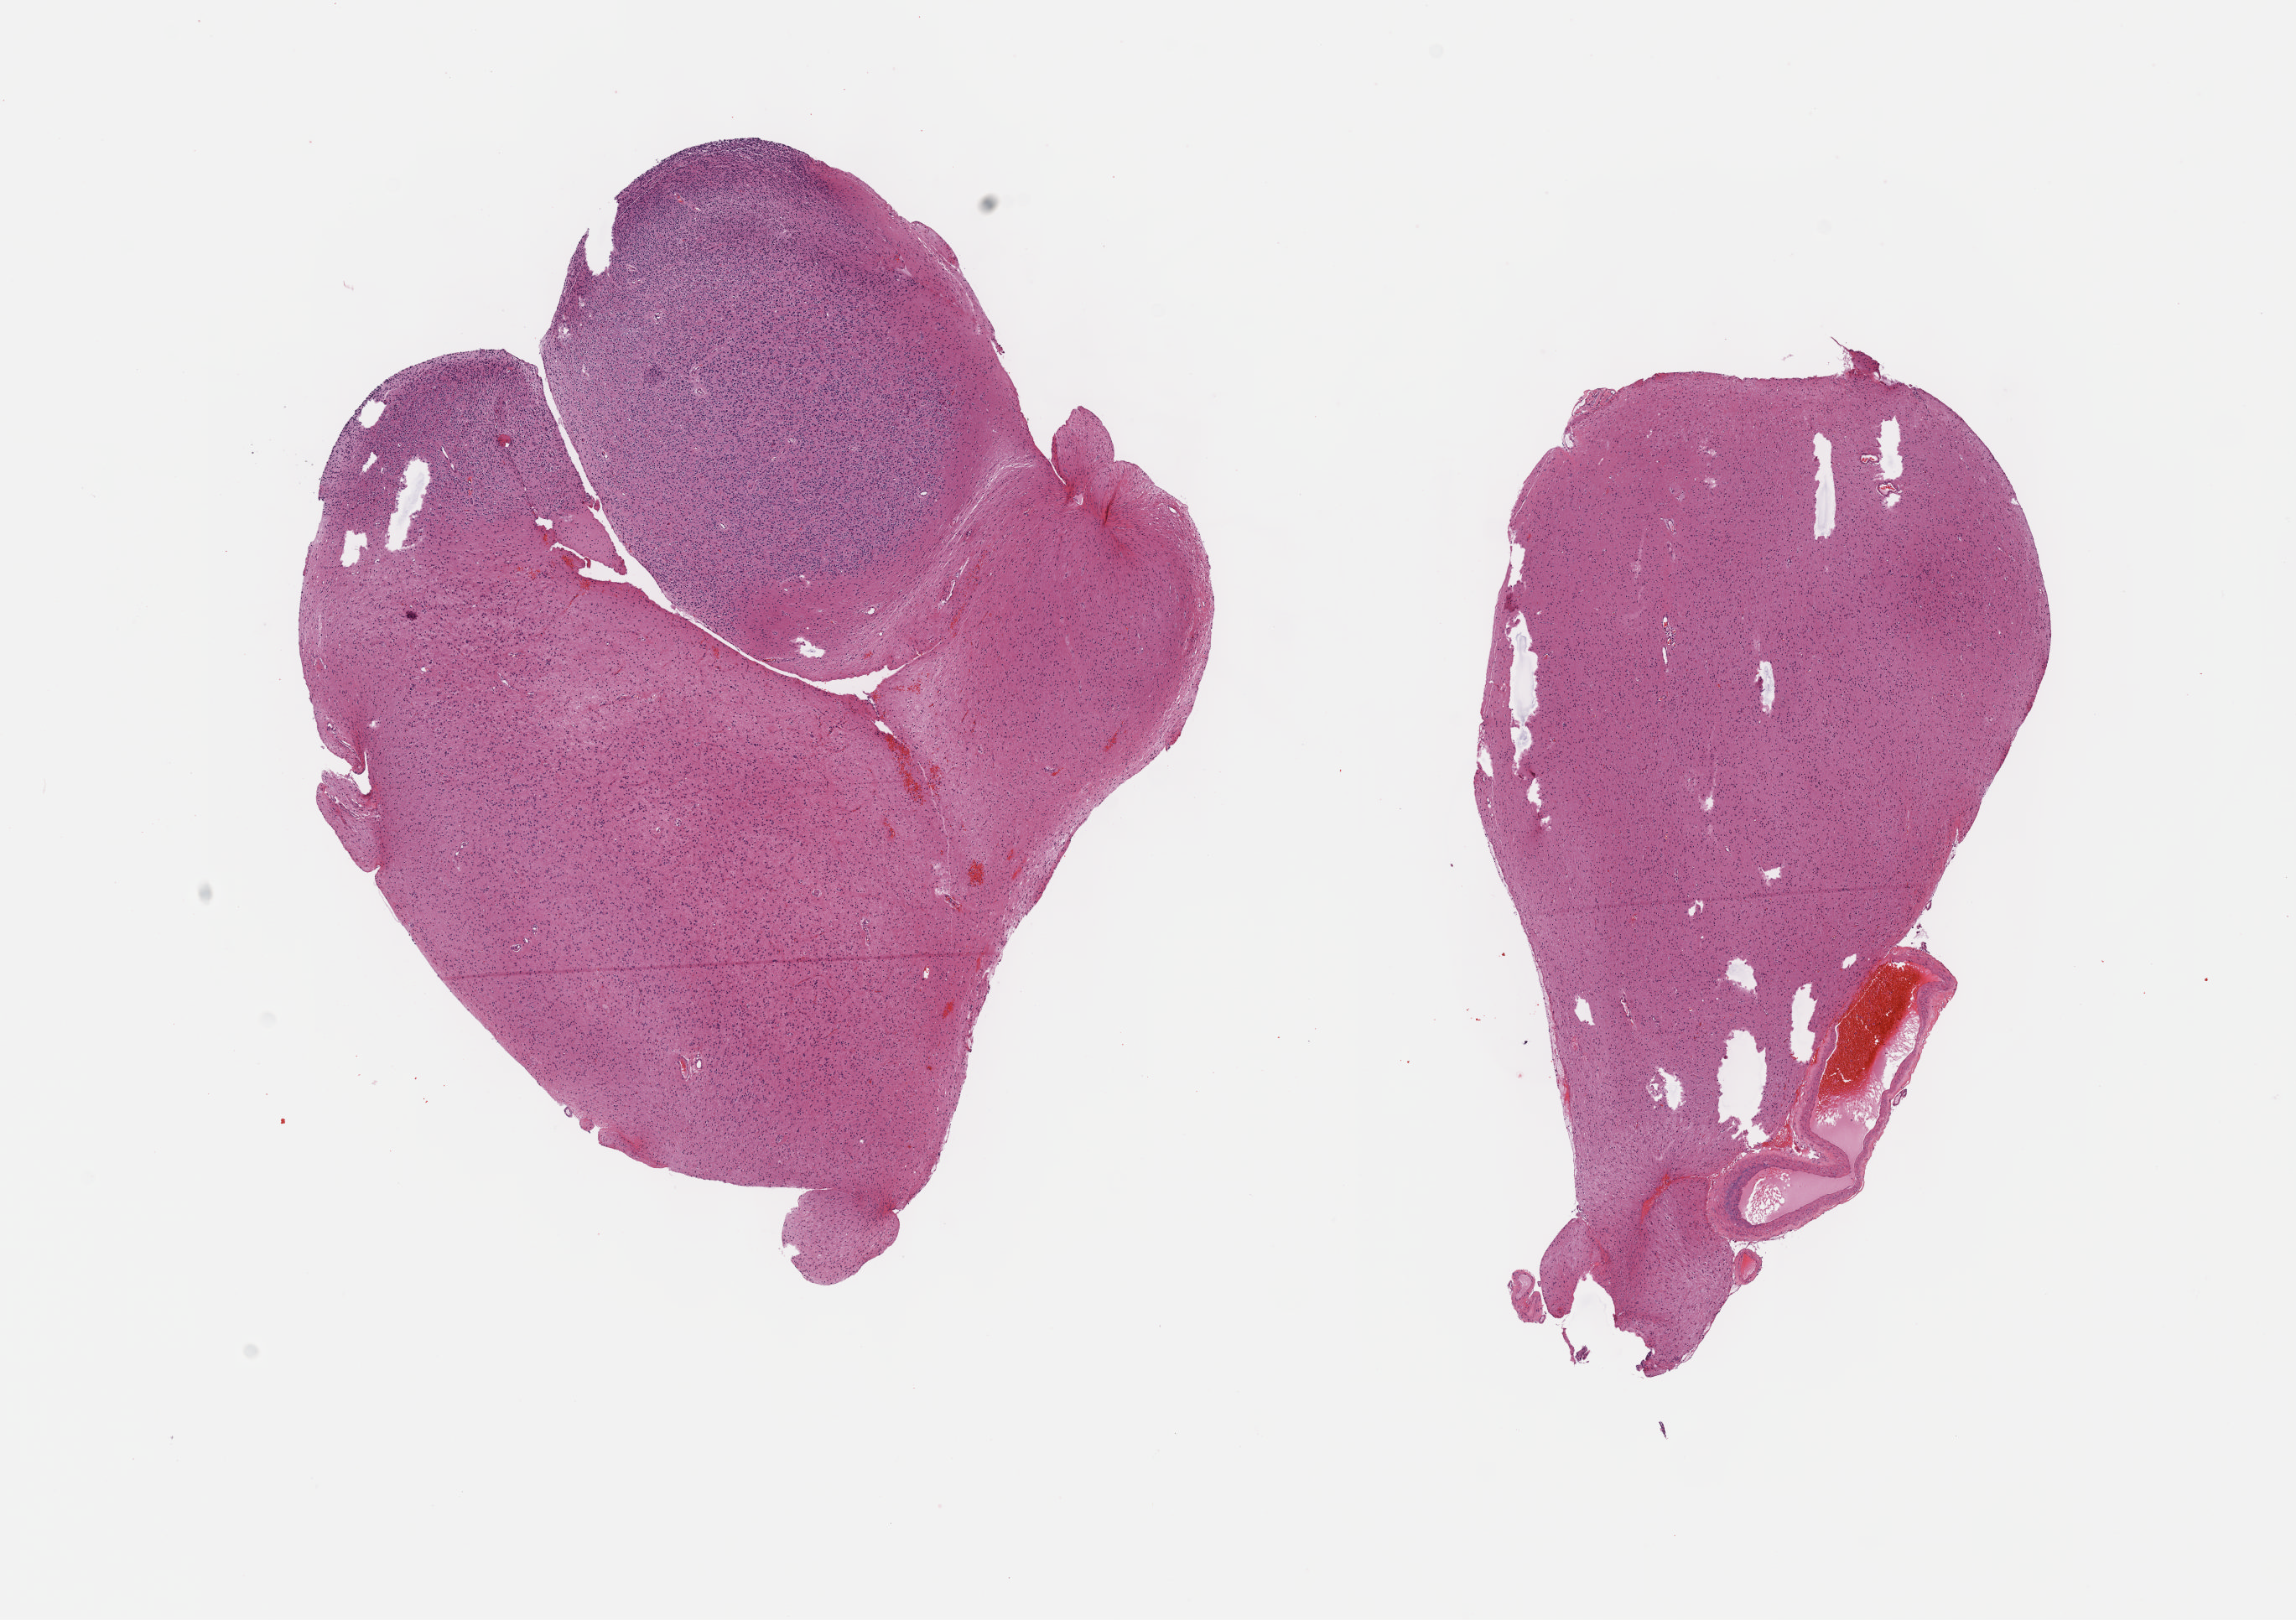
Digitized H&E tissue section (whole slide) — shown as a low-resolution overview of the whole scanned area (about 11.1 x 7.8 mm, from a 40x scan). Formalin-fixed paraffin-embedded (FFPE) diagnostic section. Sample: primary tumour, brain. Male patient; age at initial diagnosis 53 years. Histologic grade: G3 (poorly differentiated).
Histologic diagnosis: Oligodendroglioma, anaplastic (cerebrum).